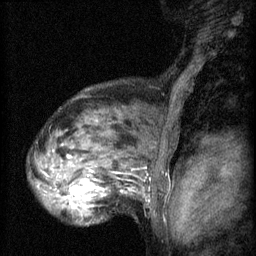
Breast MRI (dynamic contrast-enhanced), one sagittal slice. 3 images stored at this slice position (order not interpretable as contrast timing). 1.5 T. TE 4.2 ms, TR 8.2 ms. 2 mm slice thickness. 256 × 256 image matrix, field of view 180 × 180 mm. Female patient, age 48 years.
Outlined on this slice (semi-automatically segmented with operator editing):
- analysis volume of interest (the breast-tissue region the enhancement analysis was run in; not a lesion): box from (x=48, y=160) to (x=125, y=217) px
- tumour enhancement mask (voxels above the 70 % enhancement threshold inside the analysis volume of interest): (x=62, y=186)–(x=123, y=209)